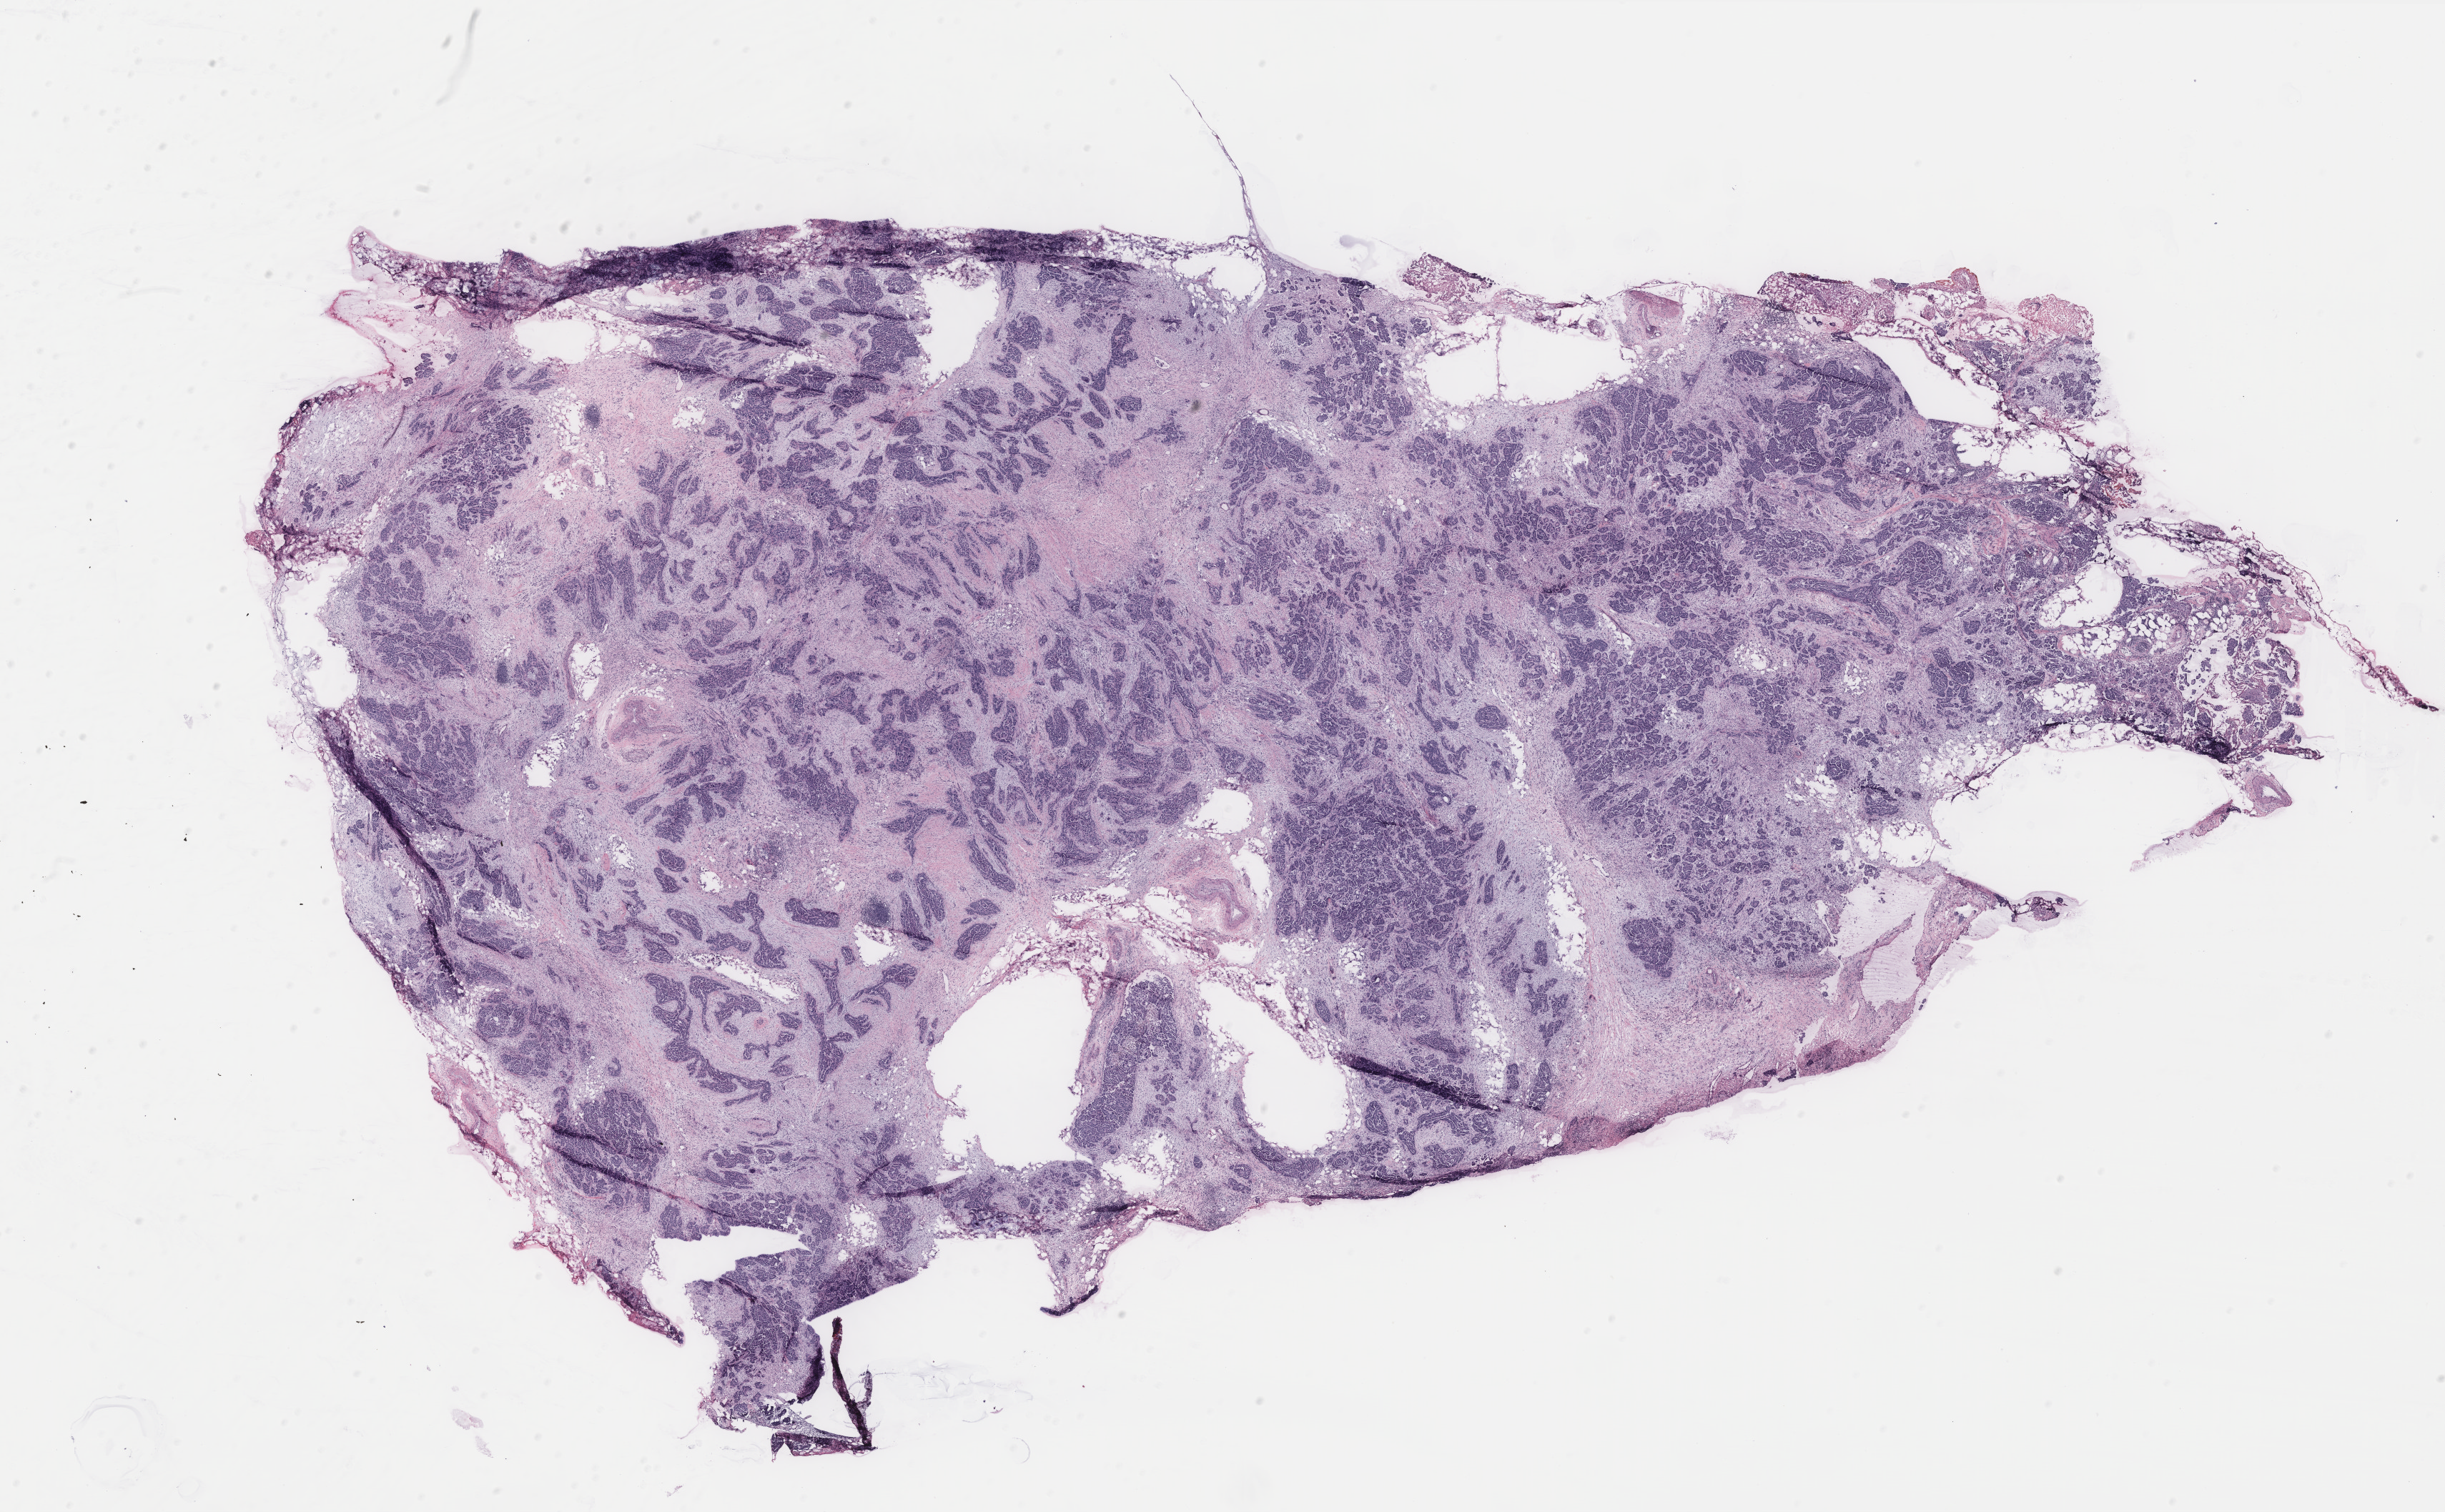
Whole-slide histology image, H&E-stained — shown as a low-resolution overview of the whole scanned area (about 27.4 x 16.9 mm); tumour tissue sample, ovary. Patient: female, age 72 years.
Histologic diagnosis: Serous adenocarcinoma, NOS (fallopian tube). Primary tumour site (as recorded): fallopian tube.